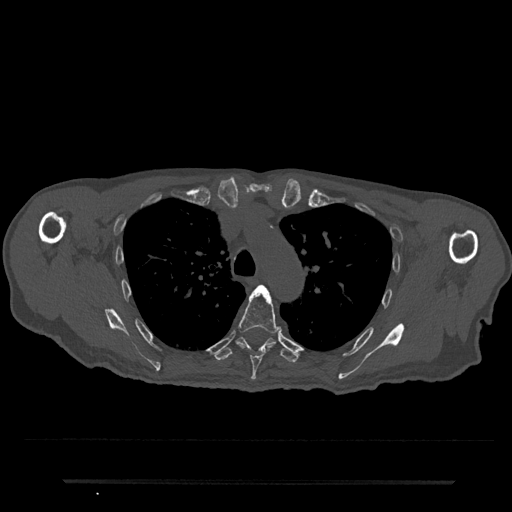
CT including the spine, one axial slice. Slice 564 of 797 in the series (ordered by position). Reconstruction kernel Br40s/3. Bone window (W 1800 / L 400 HU). 512 × 512 image matrix, field of view 427 × 427 mm. Patient: male, 74 years. Case-level facts recorded for this patient, not image findings: primary cancer: prostate.
Annotated regions visible in this slice (semi-automatically segmented with operator editing):
- T5 vertebra: bounding box [x1, y1, x2, y2] px = [238, 285, 282, 380]
- T6 vertebra: [214, 337, 298, 363]